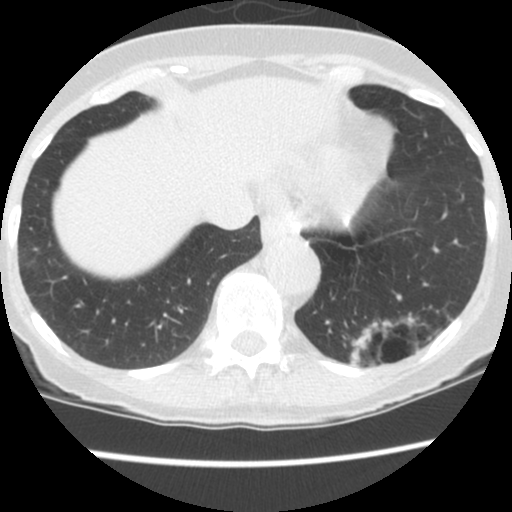
Low-dose screening chest CT, one axial slice; position 31 of 130 along the scan axis; reconstruction kernel STANDARD; lung window (W 1500 / L -600 HU); 2.5 mm slice thickness; 512 × 512 image matrix.
Outlined on this slice (manually delineated by an expert):
- lesion 1 (tumor, lower lobe of left lung): bounding box [x1, y1, x2, y2] px = [350, 321, 374, 369]